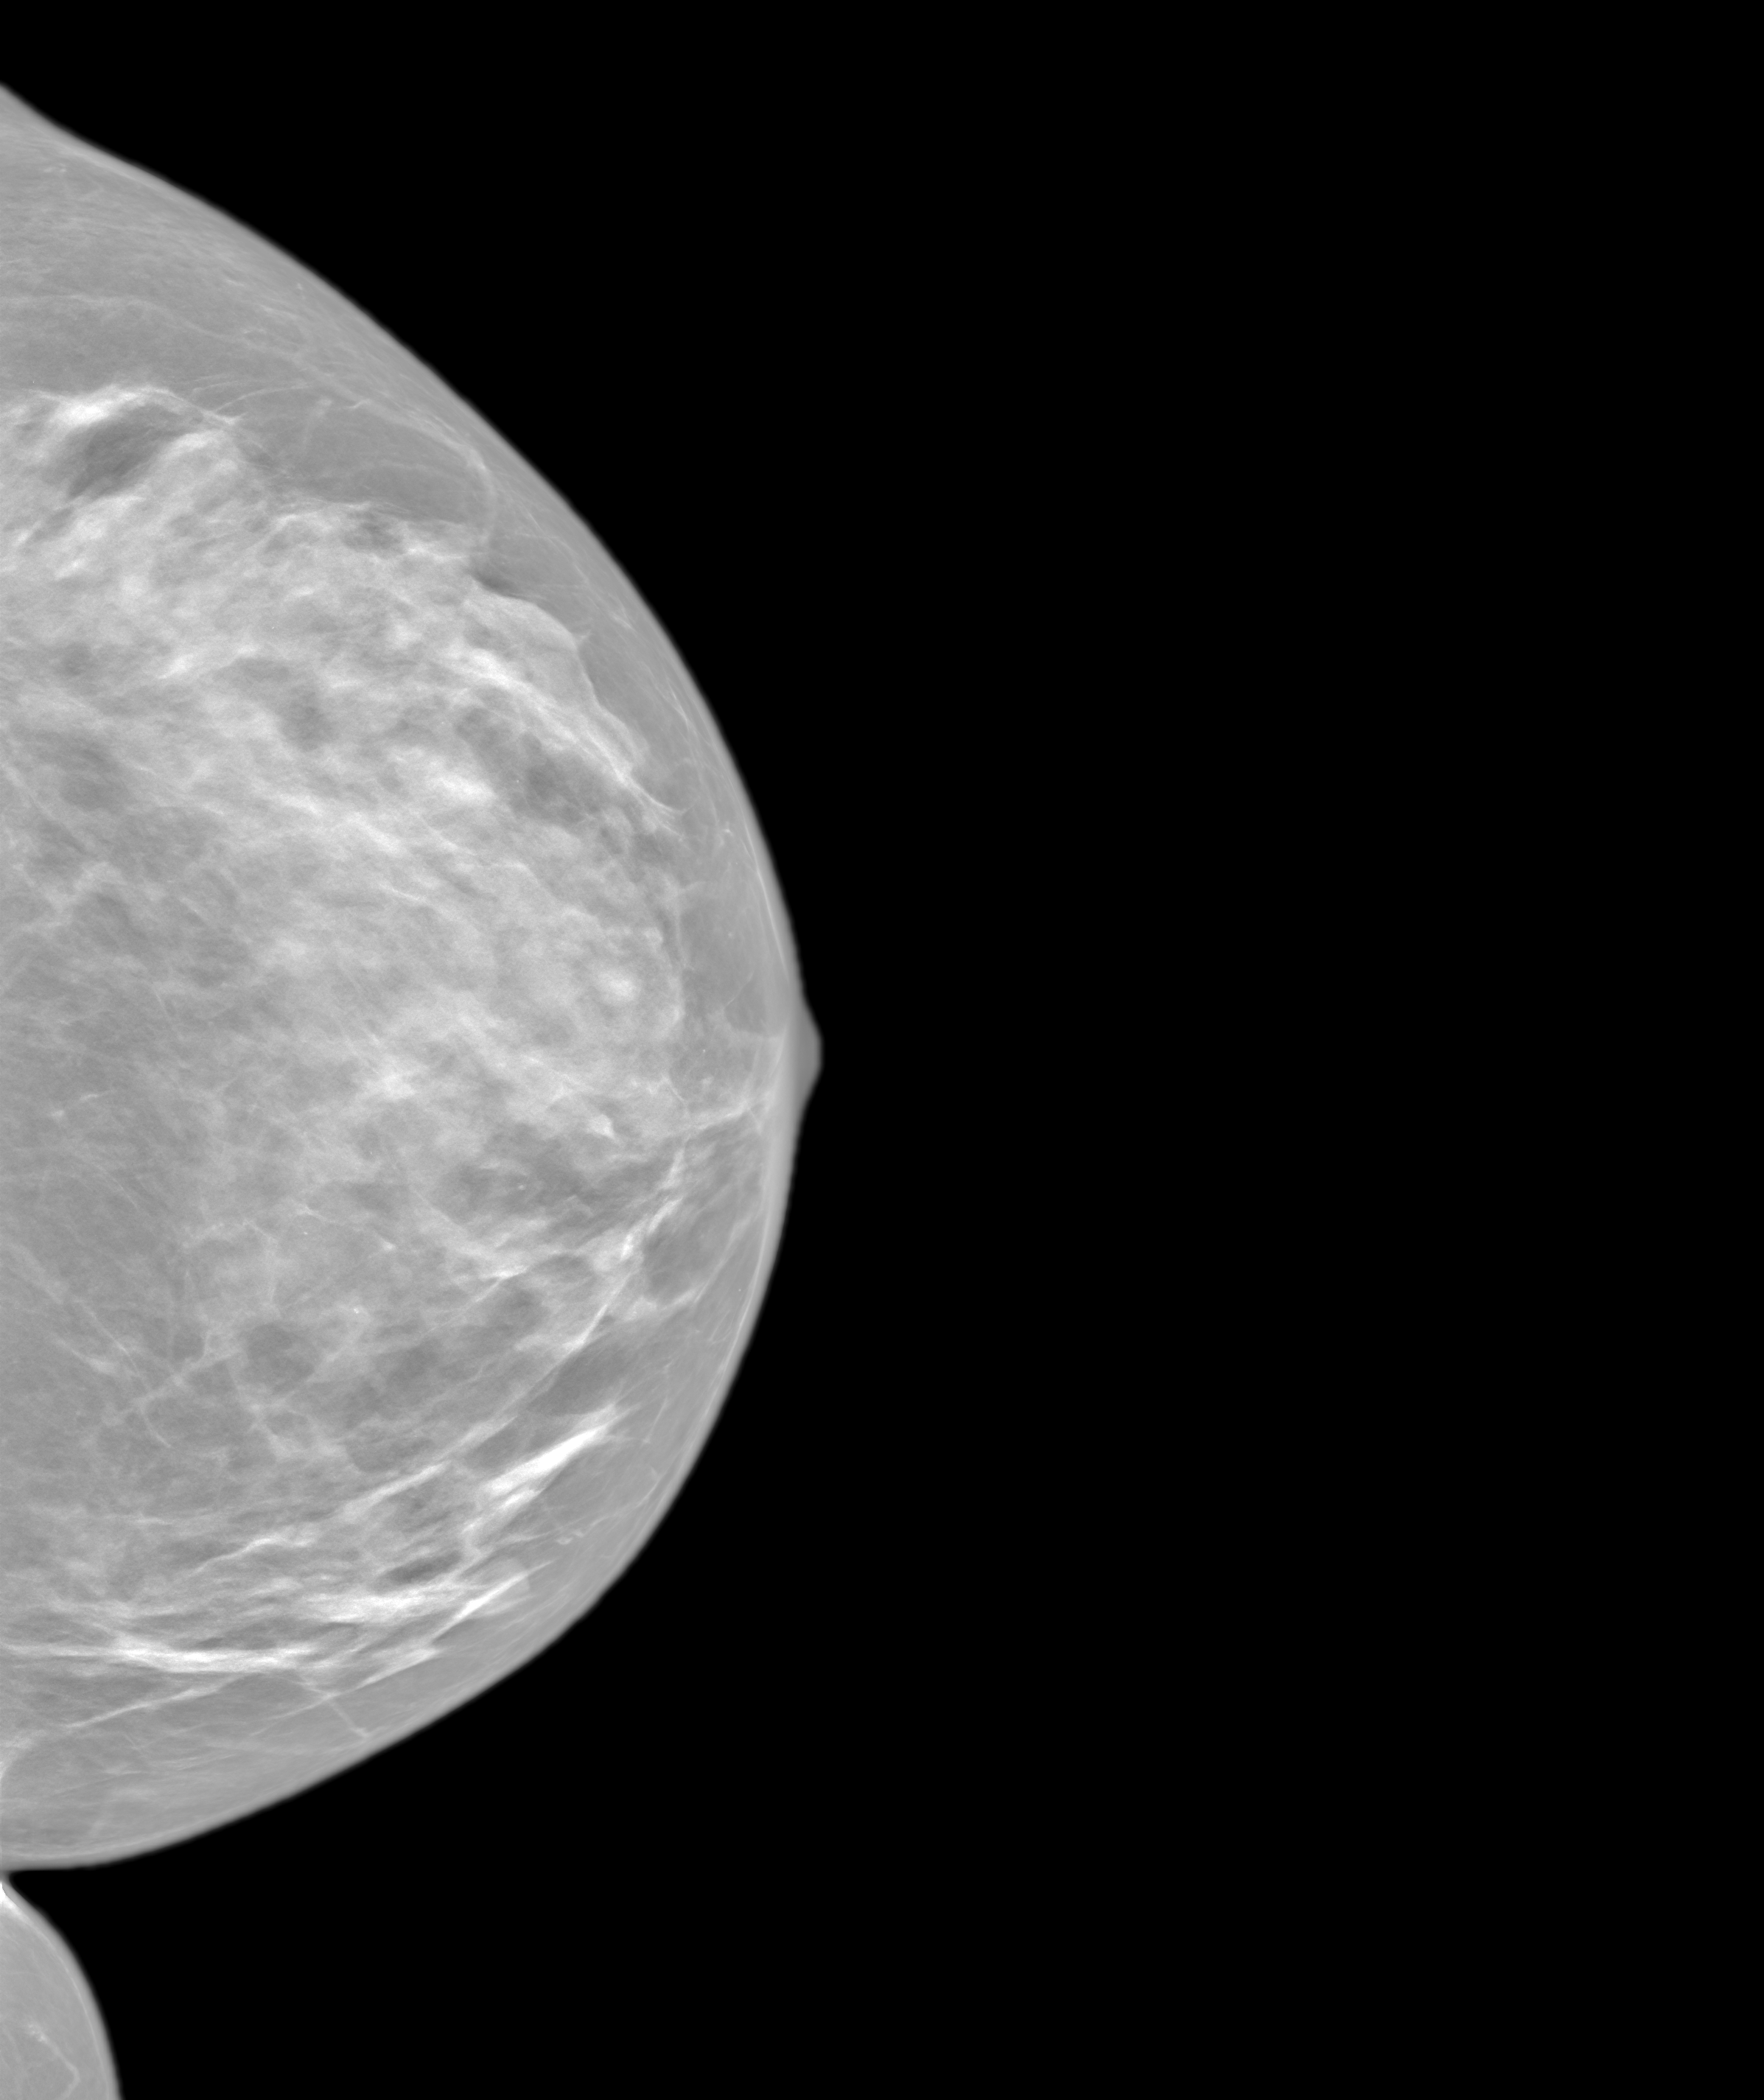
Screening examination. Female patient, age 65 years.
Image type: synthesized 2-D view from tomosynthesis. Breast: left. Projection: craniocaudal (CC) view.